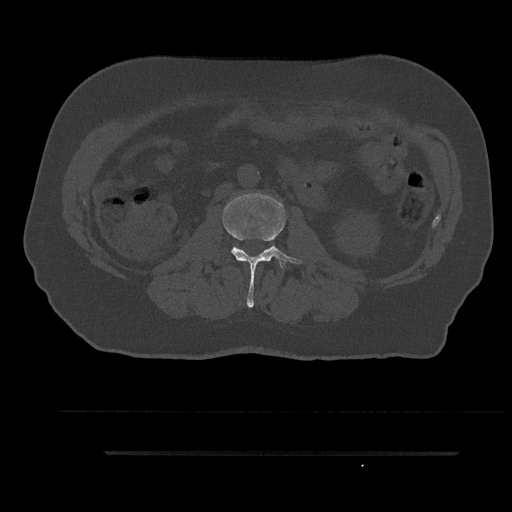
CT including the spine, one axial slice; slice 100 of 797 in the series (ordered by position); reconstruction kernel Br40s/3; 120 kVp; bone window (W 1800 / L 400 HU); 512 × 512 image matrix, field of view 432 × 432 mm. Male patient, age 63 years. From the clinical record (not read from this slice): primary cancer: renal; vertebrae with lytic lesions (as recorded): T8.
Structures marked on this image (semi-automatic segmentation, software-assisted and operator-edited):
- L2 vertebra: bounding box (x1, y1, x2, y2) in pixels: (222, 194, 302, 308)